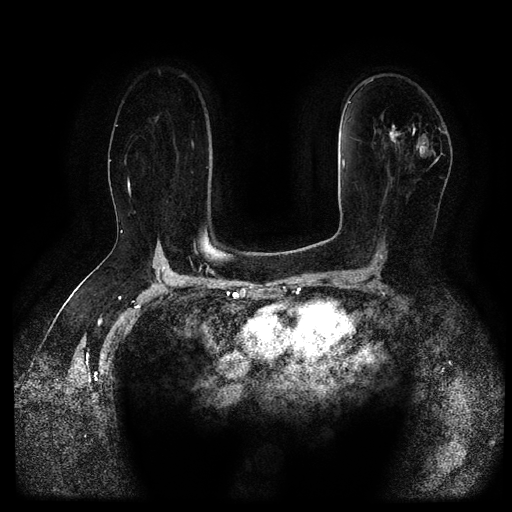
Breast MRI (dynamic contrast-enhanced, multi-phase), one axial slice; position 66 of 116 along the scan axis; dynamic contrast-enhanced series, time point 2 of 5 at this slice position (early post-contrast); 1.5 T; TE 2.6 ms, TR 5.3 ms; 512 × 512 image matrix, field of view 360 × 360 mm. Patient: female, 67 years.
Structures marked on this image (semi-automatic segmentation, software-assisted and operator-edited):
- breast lesion (labelled 'tumour' in the annotation; benign lesions carry a separate 'benign' label): box from (x=388, y=123) to (x=417, y=152) px